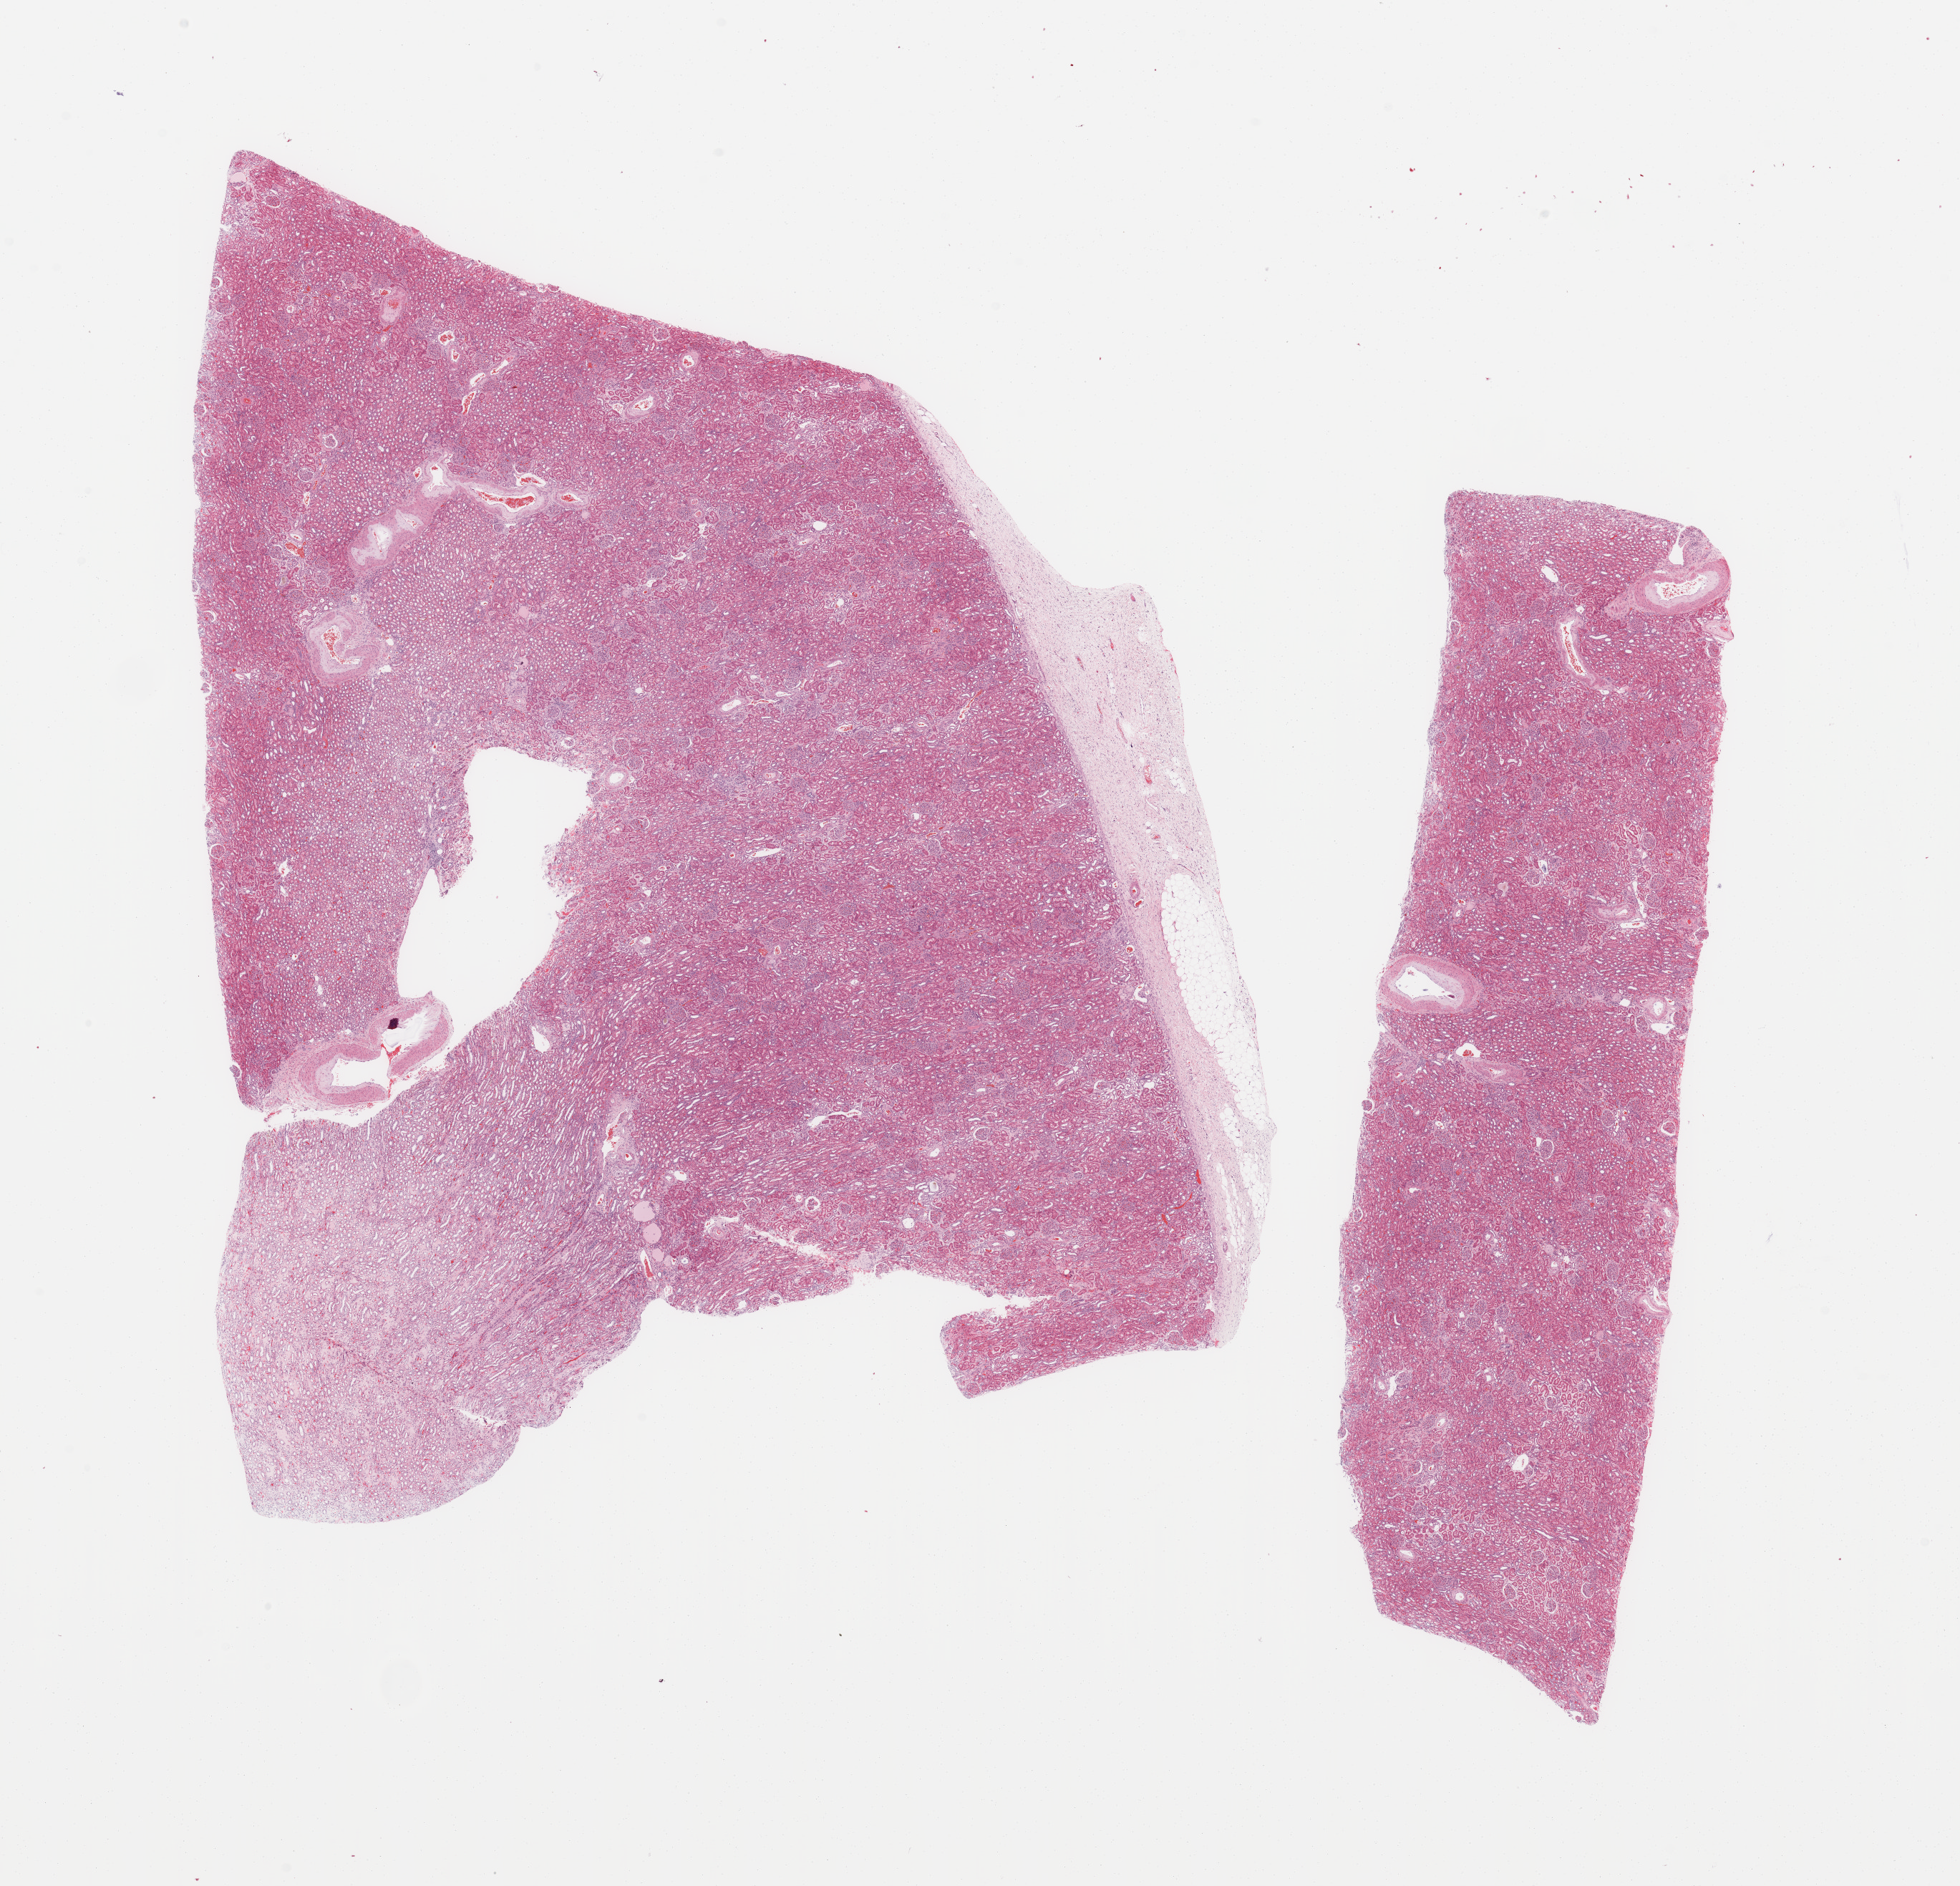
Whole-slide histology image, Hematoxylin and eosin (H&E) stained — a low-resolution overview of the entire scanned area, about 21.7 x 20.8 mm (acquisition: 20x scan), normal (non-tumour) tissue sample, sampled site: kidney. Patient: male, age 69 years.
• this section: normal (non-tumour) tissue from the same patient
• patient diagnosis: Renal cell carcinoma, NOS